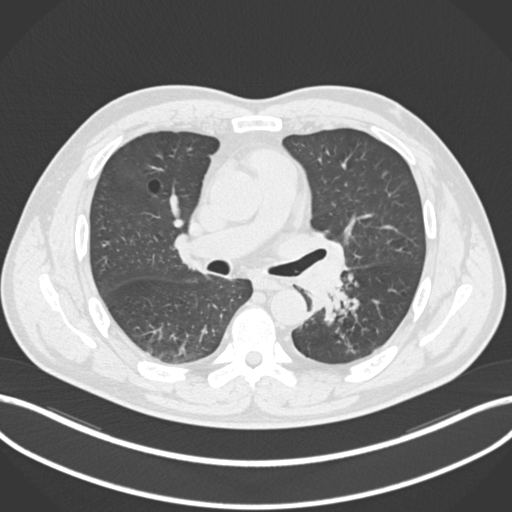
Chest CT, one axial slice. Position 131 of 223 along the scan axis. Reconstruction kernel B30f. Lung window (W 1500 / L -600 HU). 1 mm slice thickness. 512 × 512 image matrix, field of view 400 × 400 mm. Male patient, age 50 years. Case-level facts recorded for this patient, not image findings: clinical TNM (as recorded): T2a N3 M0.
Annotated regions visible in this slice (bounding box drawn by a radiologist):
- lung tumour (recorded histology: squamous cell carcinoma): box from (x=288, y=247) to (x=353, y=319) px